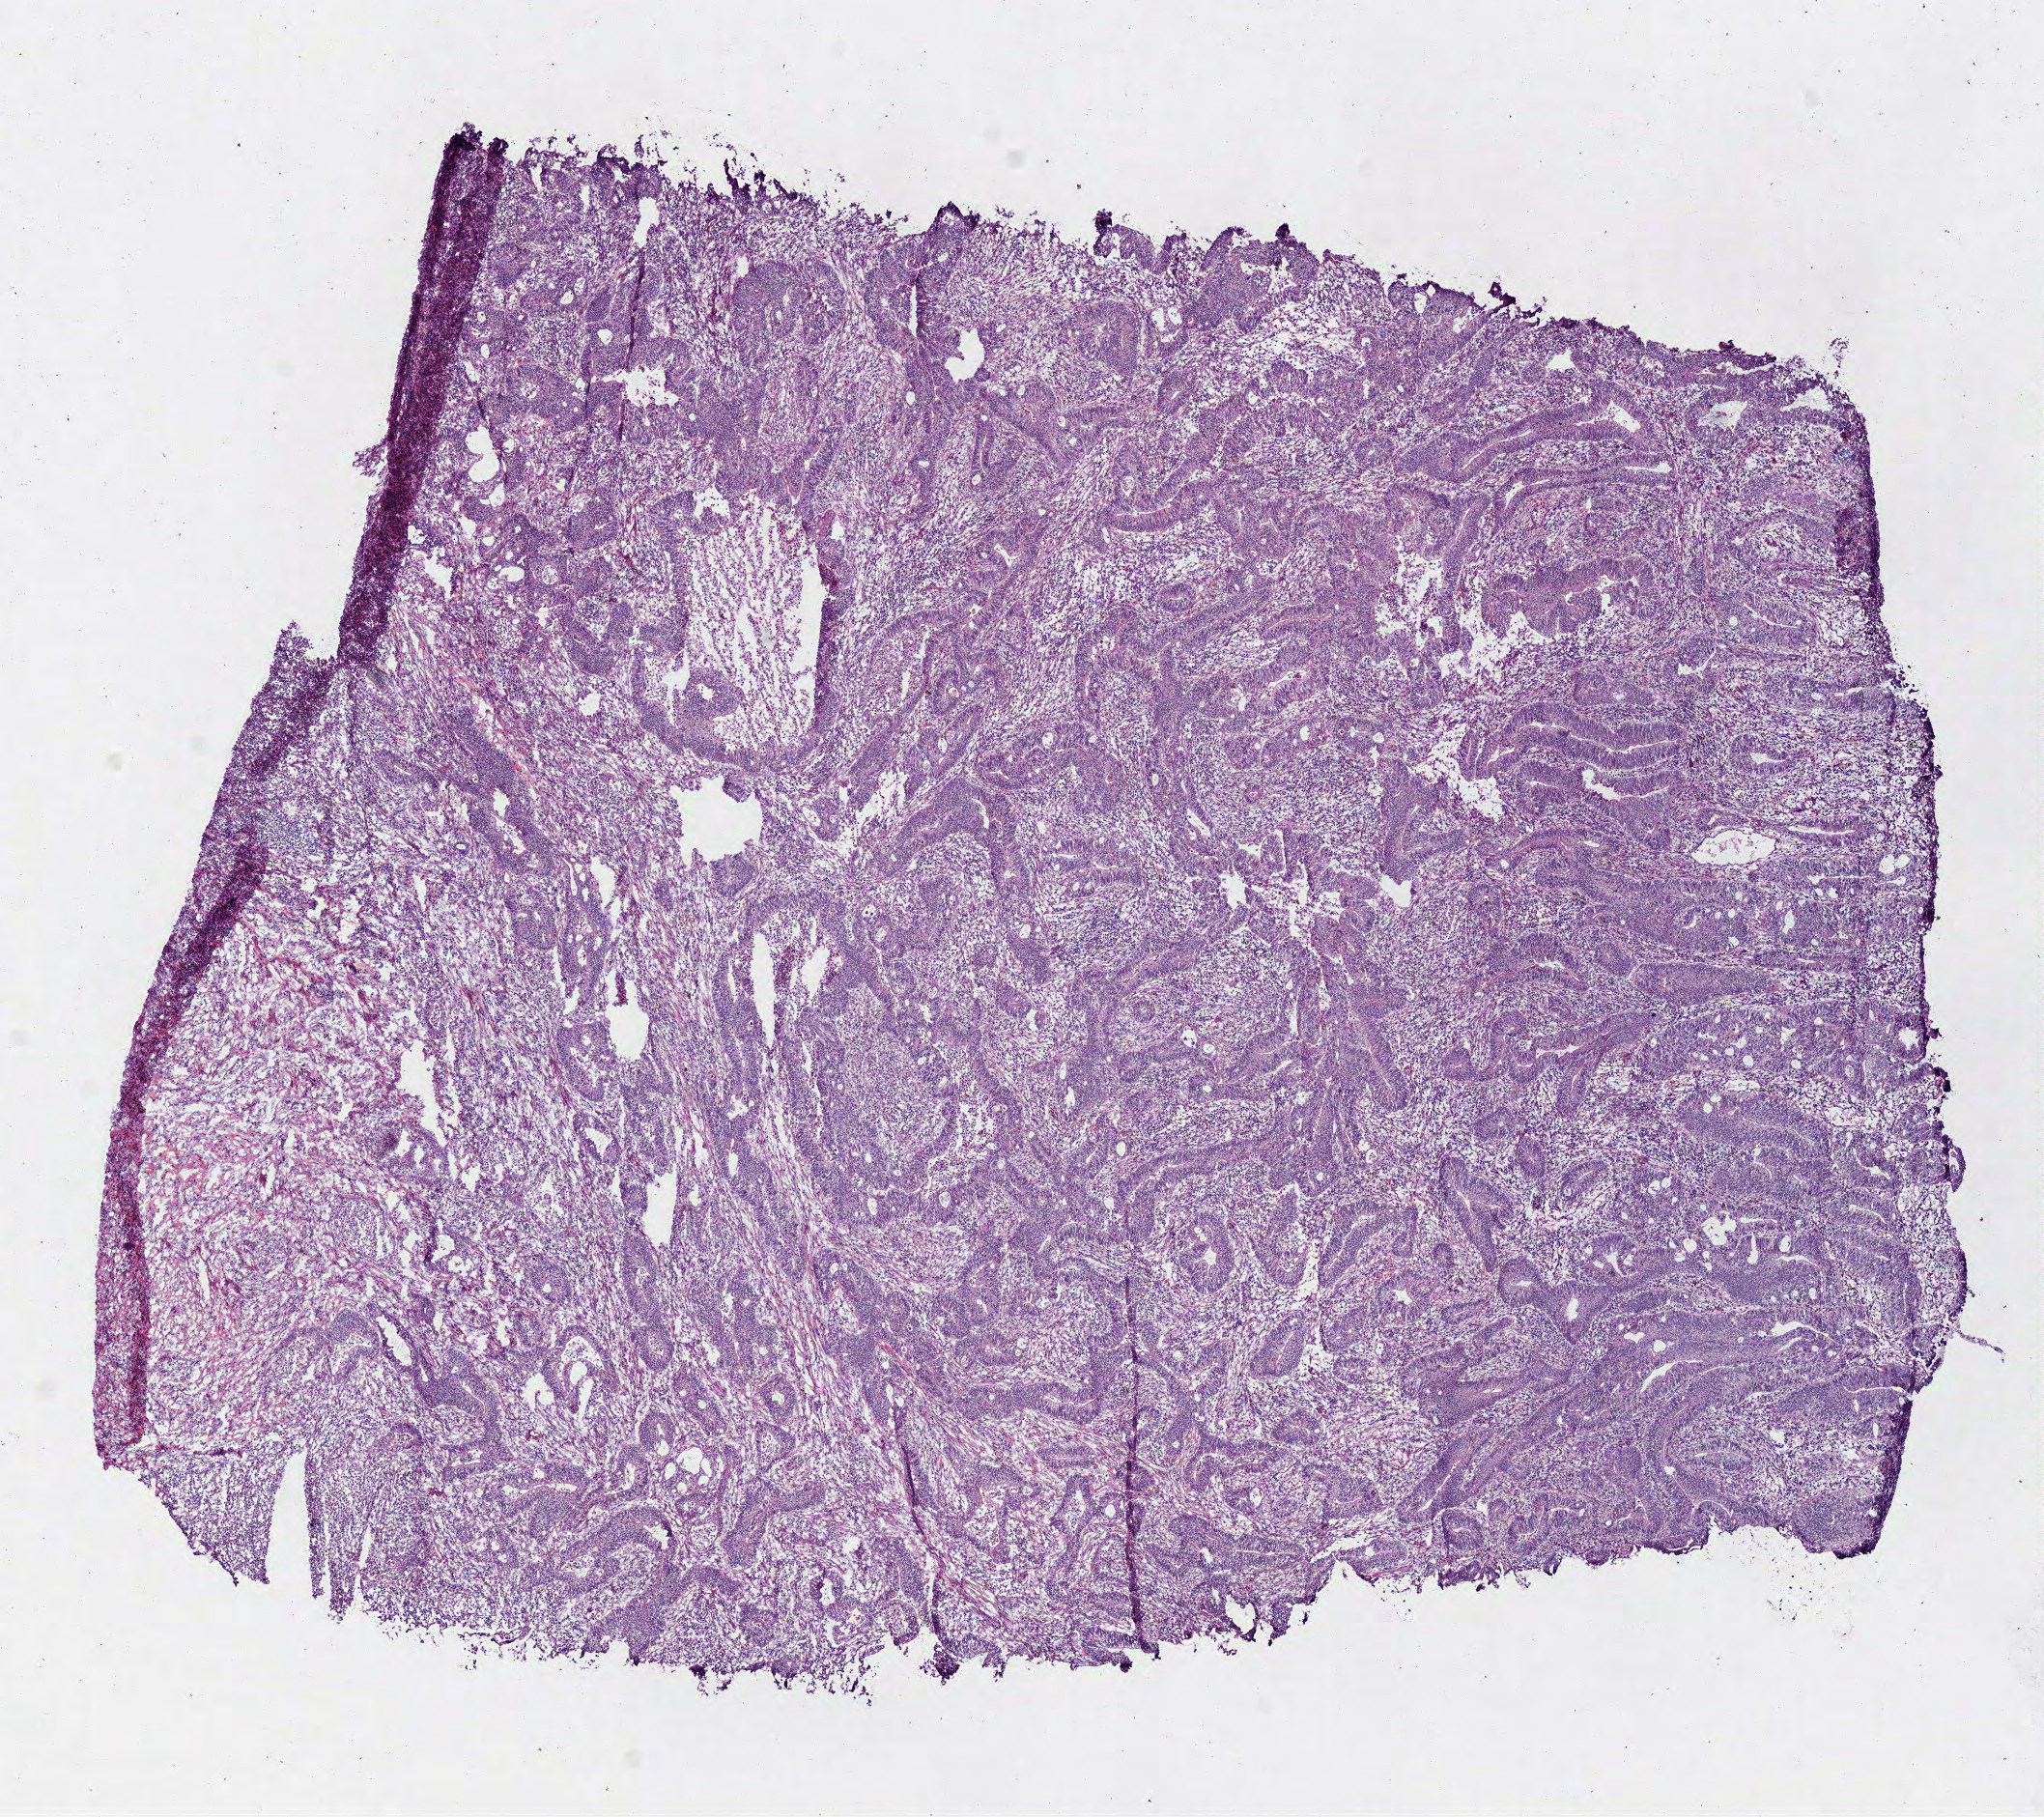
H&E whole-slide image — a low-resolution overview of the entire scanned area, about 8.3 x 7.4 mm (slide scanned at 40x), frozen section from the bottom of the tissue portion, colon, primary tumour sample. Male, age 69 years at initial diagnosis.
Histologic diagnosis: Adenocarcinoma, NOS.